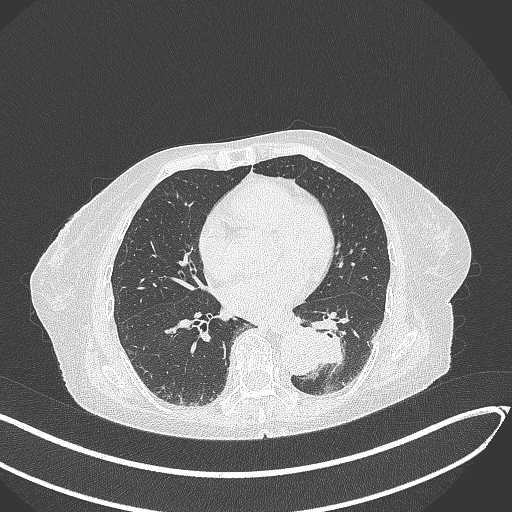
Chest CT, one axial slice; position 105 of 324 along the scan axis; reconstruction kernel B70f; 120 kVp; lung window (W 1500 / L -600 HU); 1 mm slice thickness; 512 × 512 image matrix, field of view 400 × 400 mm. Female patient, age 82 years. Case-level facts recorded for this patient, not image findings: clinical TNM (as recorded): T1b N0 M1.
Annotated regions visible in this slice (bounding box drawn by a radiologist):
- lung tumour (recorded histology: adenocarcinoma): box from (x=298, y=321) to (x=349, y=369) px